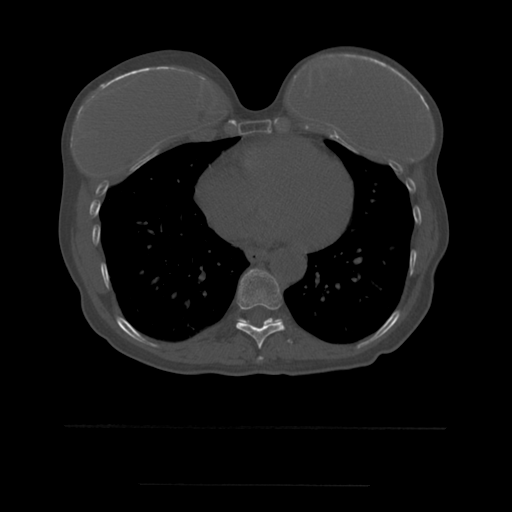
CT including the spine, one axial slice; slice 317 of 544 in the series (ordered by position); bone window (W 1800 / L 400 HU); 512 × 512 image matrix, field of view 350 × 350 mm. Patient age 58 years. From the clinical record (not read from this slice): primary cancer: lung.
Structures marked on this image (semi-automatically segmented with operator editing):
- T10 vertebra: bounding box <241,319,248,322> (left, top, right, bottom; pixels)
- T8 vertebra: <258,357,263,360>
- T9 vertebra: <236,269,291,349>